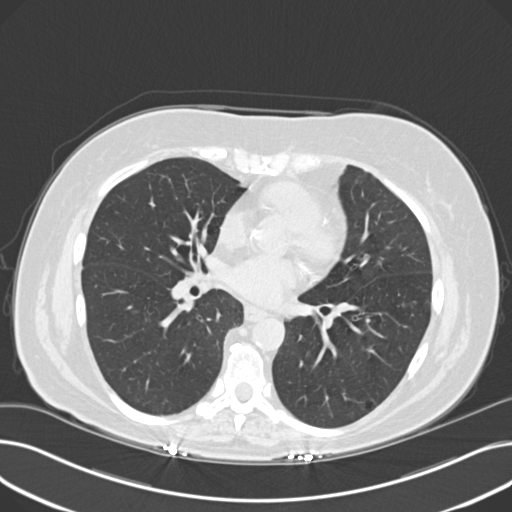
Low-dose screening chest CT, one axial slice. Position 94 of 203 along the scan axis. Reconstruction kernel B30f. 120 kVp. Lung window (W 1500 / L -600 HU). 2 mm slice thickness. 512 × 512 image matrix, field of view 372 × 372 mm.
Structures marked on this image (manually delineated by an expert):
- lesion 1 (tumor, upper lobe of left lung): box from (x=377, y=257) to (x=385, y=267) px